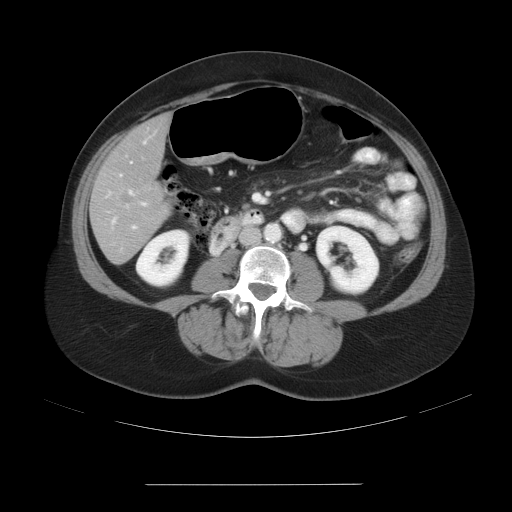
Contrast-enhanced abdominal CT, one axial slice. Slice 7 of 27 in the series (ordered by position). Soft-tissue window (W 400 / L 40 HU). 7.5 mm slice thickness. 512 × 512 image matrix, field of view 440 × 440 mm. Female patient, age 58 years. Case-level facts recorded for this patient, not image findings: diagnosis: colorectal cancer liver metastases, imaged before liver resection; multiple liver metastases: yes; largest metastasis: 1.9 cm.
Annotated regions visible in this slice (manually delineated by an expert):
- hepatic veins: bounding box (x1, y1, x2, y2) in pixels: (129, 191, 133, 195)
- liver: (92, 116, 169, 263)
- planned liver remnant (the part of the liver to remain after resection): (96, 116, 169, 191)
- portal vein (with intrahepatic branches): (111, 131, 156, 229)